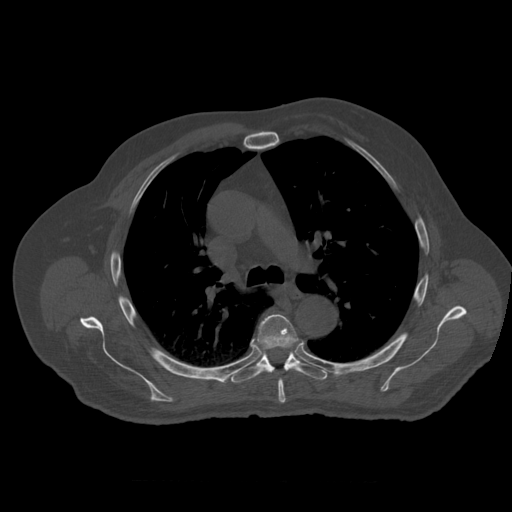
CT including the spine, one axial slice; position 391 of 399 along the scan axis; reconstruction kernel STANDARD; 120 kVp; bone window (W 1800 / L 400 HU); 1.25 mm slice thickness; 512 × 512 image matrix, field of view 407 × 407 mm. Patient age 73 years. Case-level facts recorded for this patient, not image findings: primary cancer: prostate; vertebrae with lytic lesions (as recorded): L2.
Outlined on this slice (semi-automatic segmentation, software-assisted and operator-edited):
- T5 vertebra: bounding box (x1, y1, x2, y2) in pixels: (257, 315, 299, 403)
- T6 vertebra: (231, 344, 327, 383)